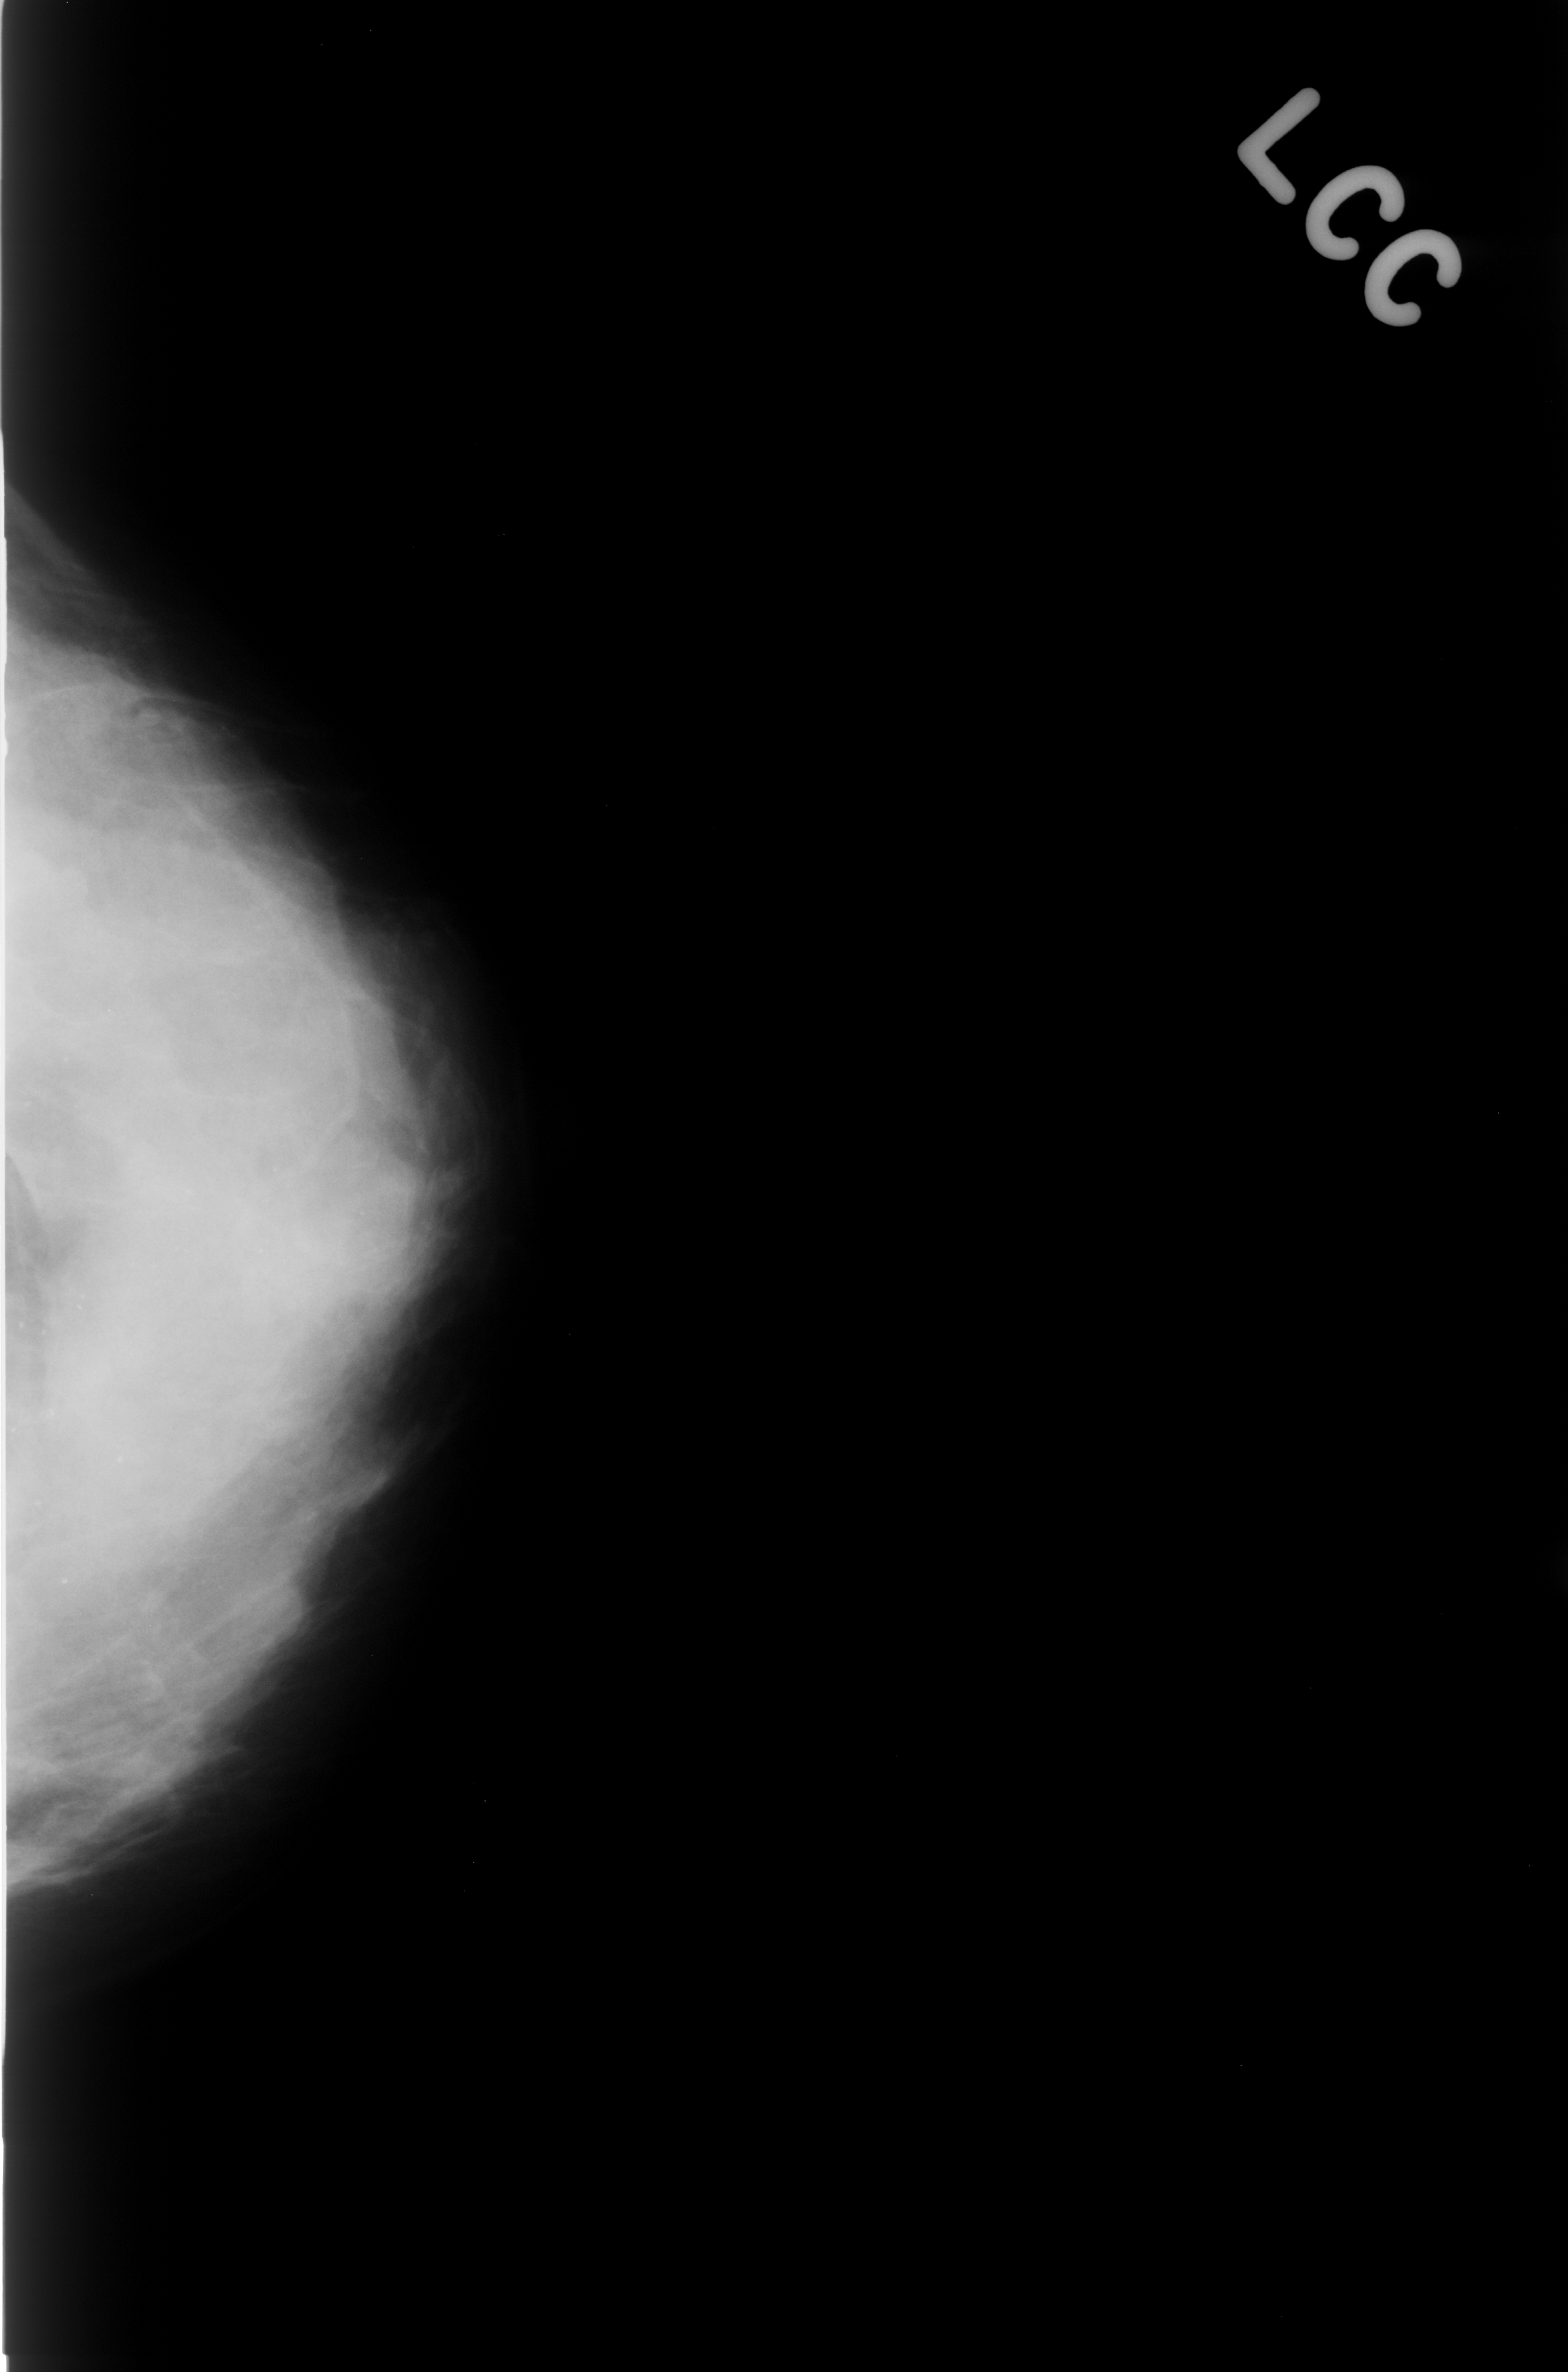
Scanned film-screen mammogram; left breast; CC view; BI-RADS breast density category 4 (scale 1–4).
- Marked findings (only marked abnormalities are described; nothing is implied about the rest of the image): calcifications, morphology punctate, distribution diffusely scattered; BI-RADS assessment category 2; pathology (as recorded): benign.